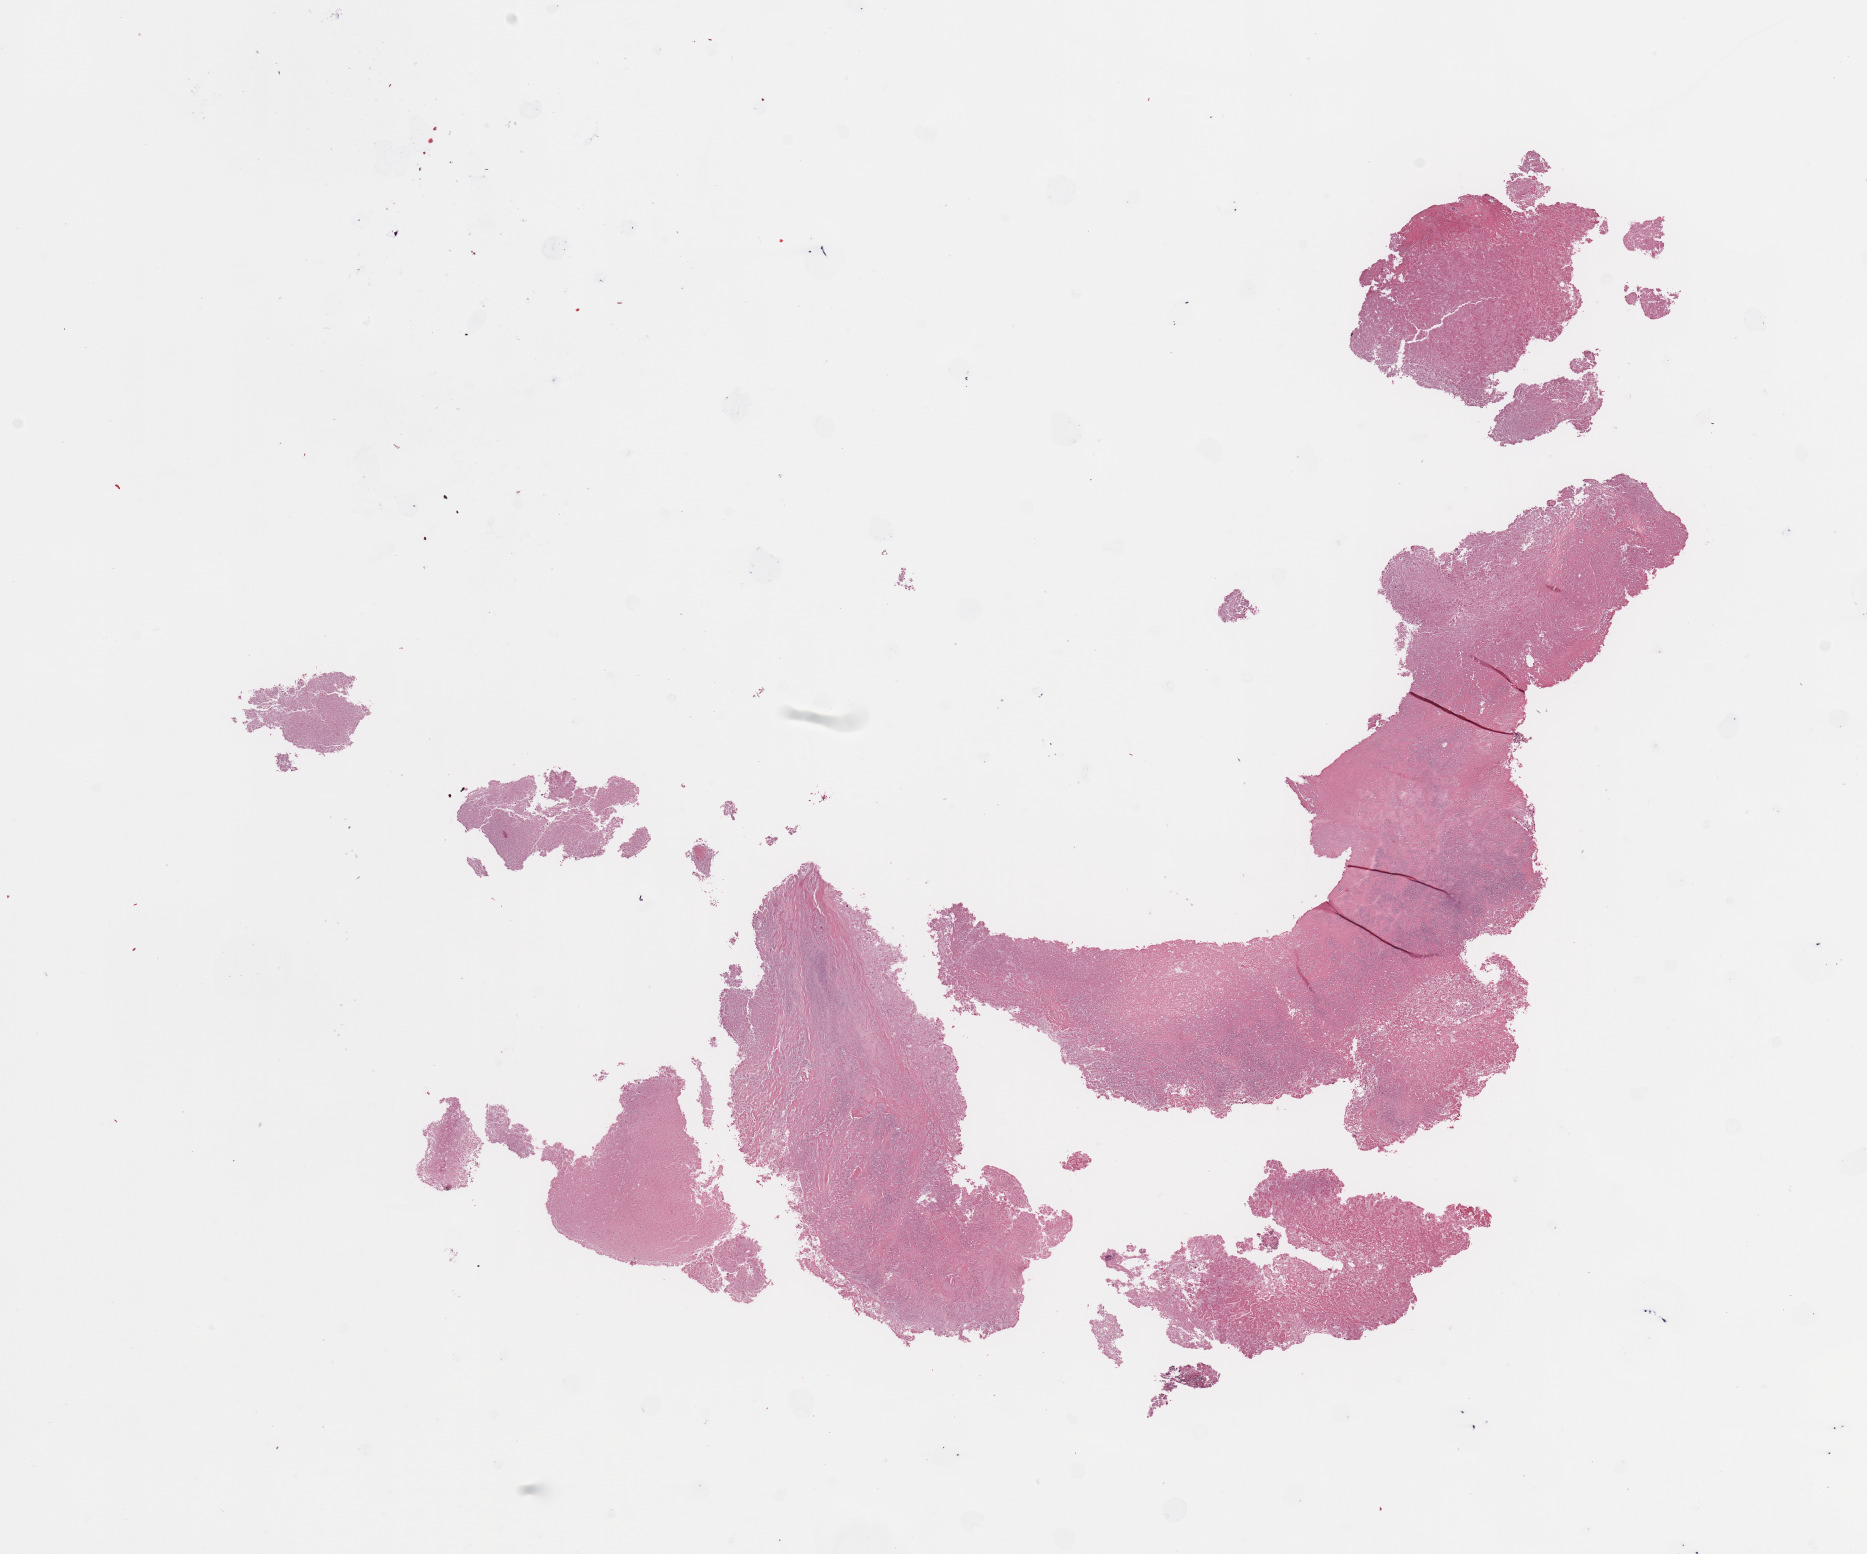
H&E-stained whole-slide image — a low-resolution overview of the entire scanned area, about 14.8 x 12.3 mm (from a 20x scan). Tumour tissue sample, kidney. Male, 53 y/o. Histologic grade: G3 (poorly differentiated).
Diagnosis: Renal cell carcinoma, NOS. Primary tumour site (as recorded): middle. AJCC pathologic stage: II.